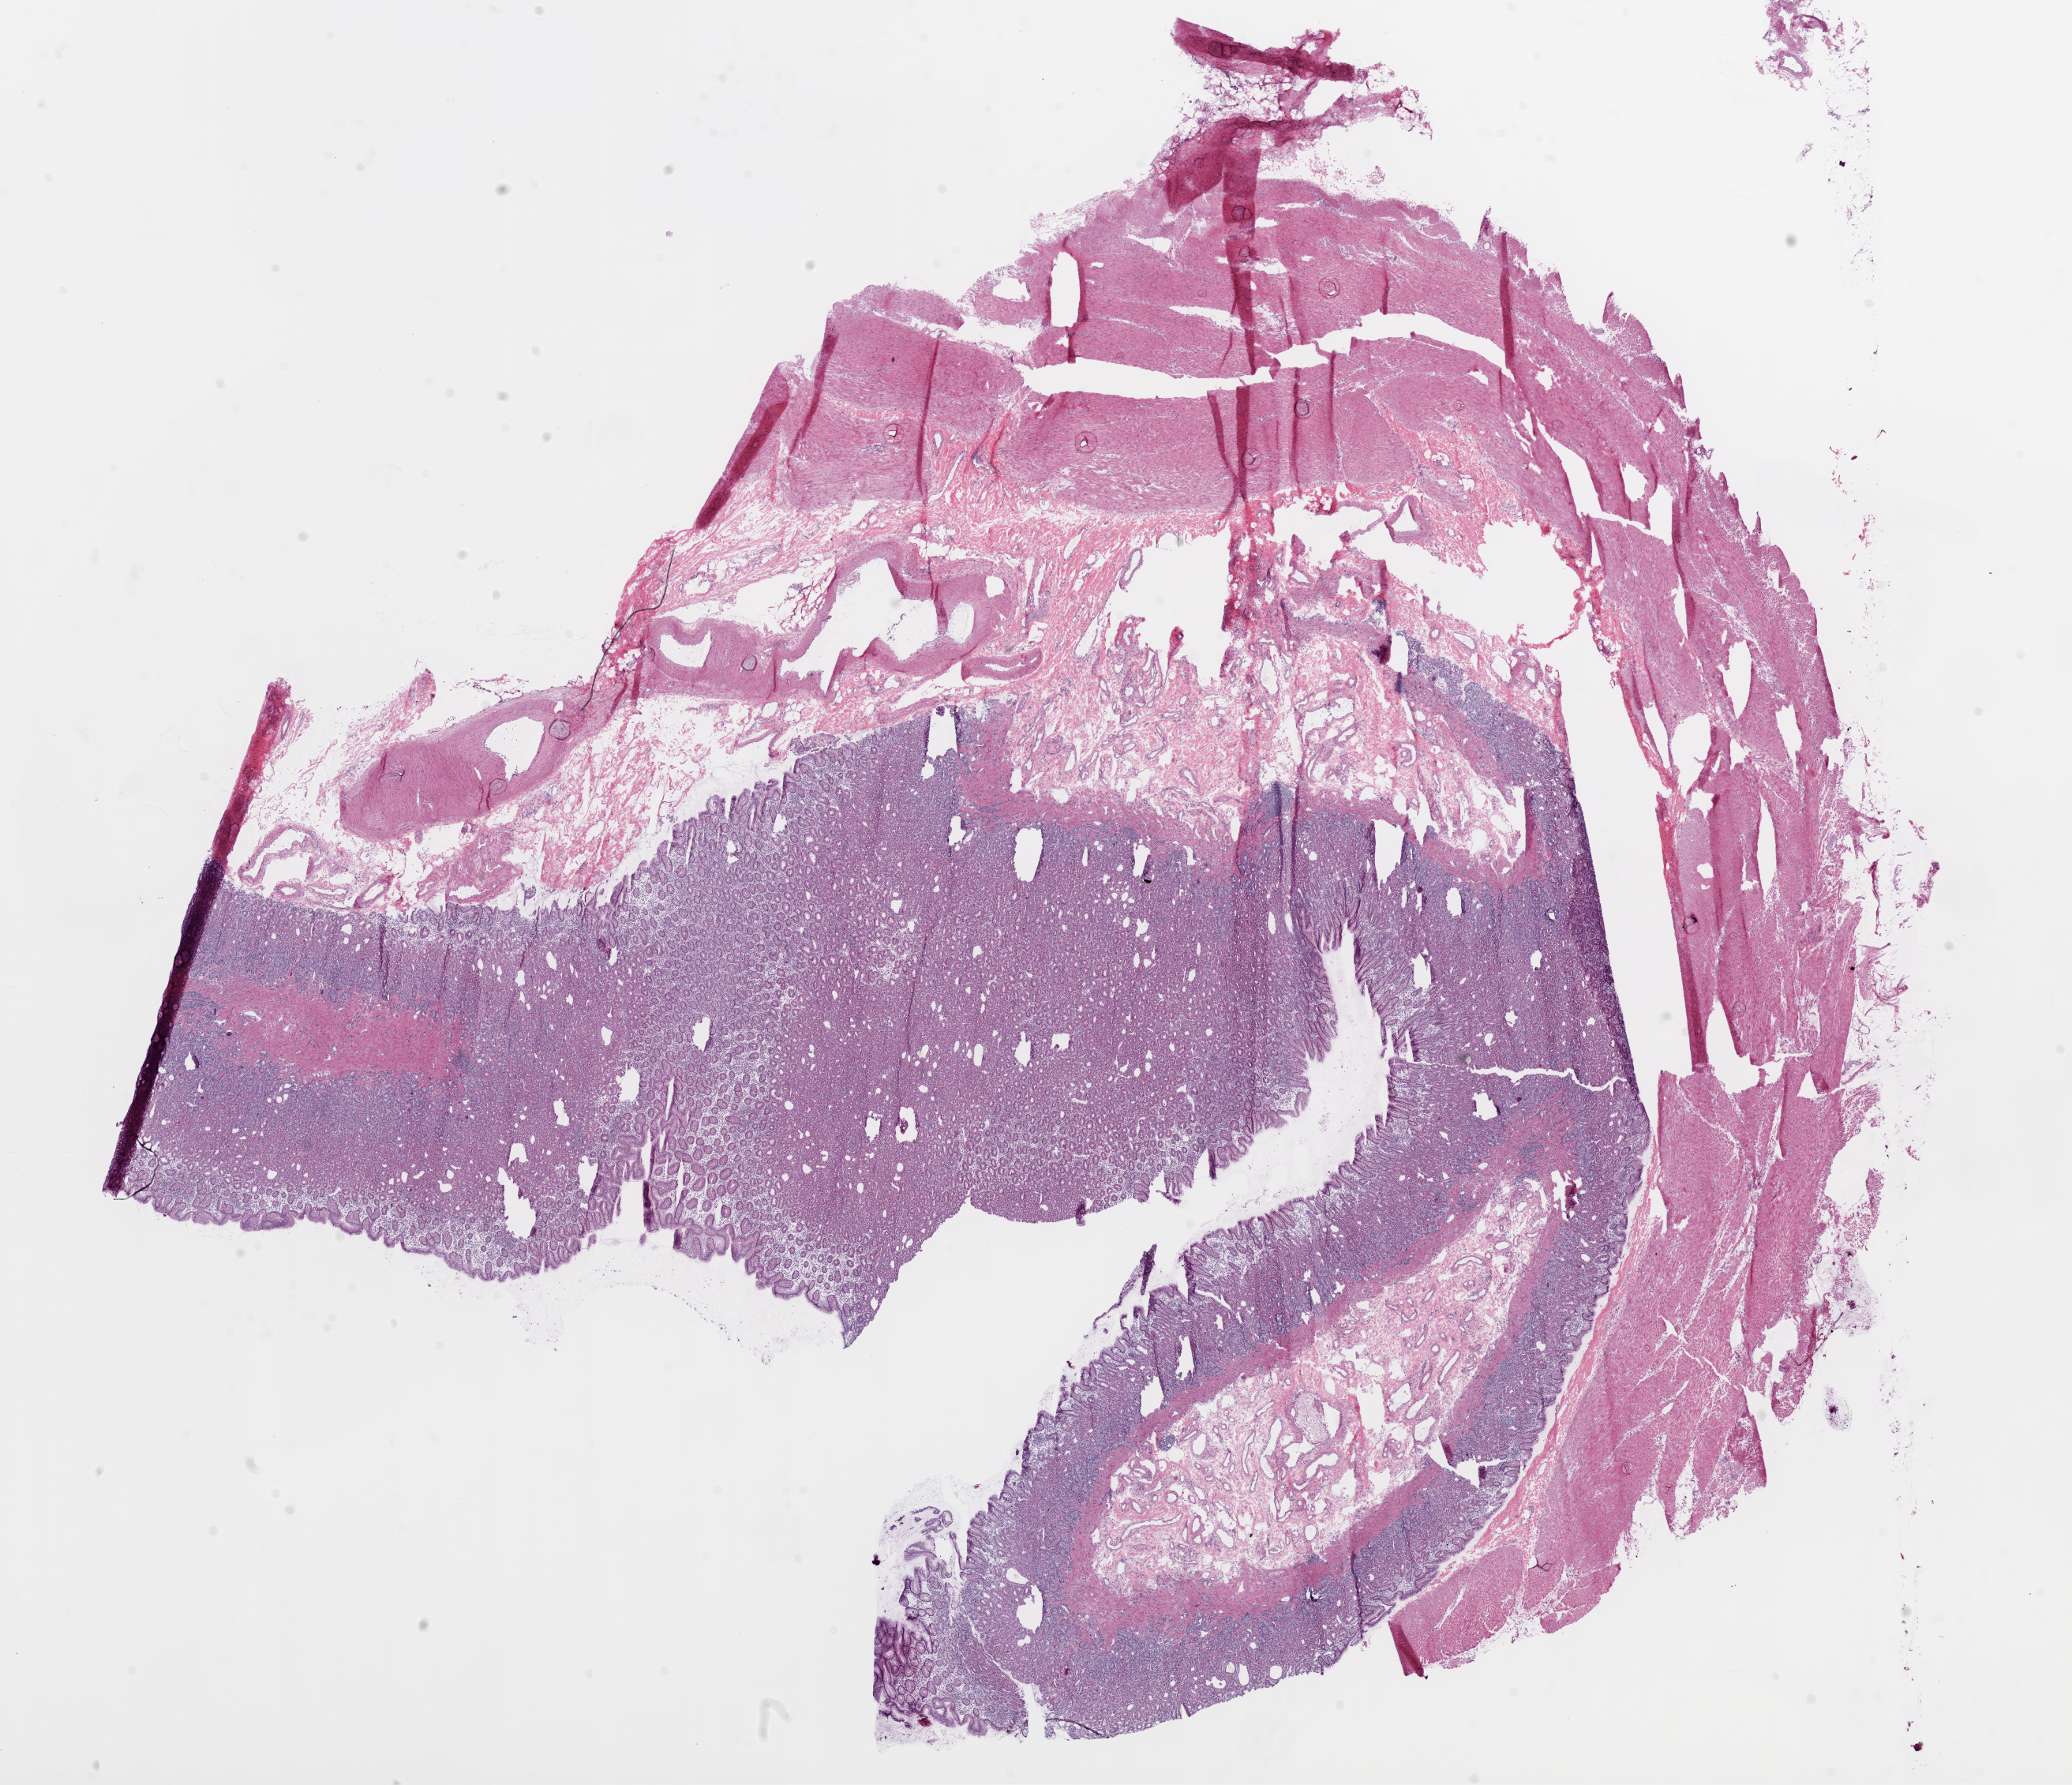
Hematoxylin and eosin (H&E) stained whole-slide image, whole scanned area (about 21.1 x 18.1 mm) shown as a low-resolution overview. Frozen section from the top of the tissue portion. Solid tissue normal (non-tumour tissue) sample from the stomach. Female patient; age at initial diagnosis 74 years.
This section: solid tissue normal sample (biorepository sample class). Patient diagnosis: Adenocarcinoma, NOS (gastric antrum).